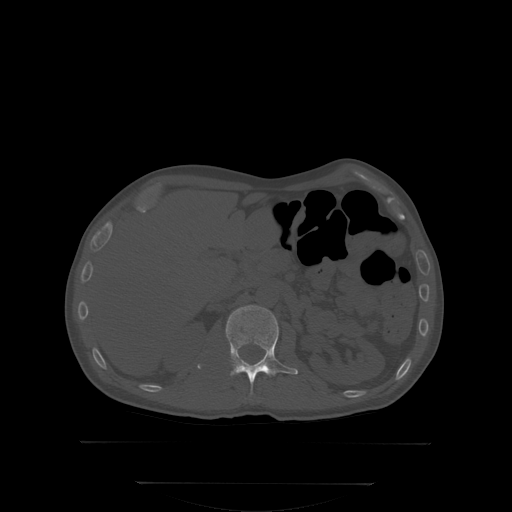
CT including the spine, one axial slice; bone window (W 1800 / L 400 HU); 512 × 512 image matrix, field of view 500 × 500 mm. Patient: male, 58 years. Case-level facts recorded for this patient, not image findings: primary cancer: prostate; vertebrae with lytic lesions (as recorded): L1.
Structures marked on this image (semi-automatically segmented with operator editing):
- L1 vertebra: bounding box (x1, y1, x2, y2) in pixels: (225, 305, 296, 384)